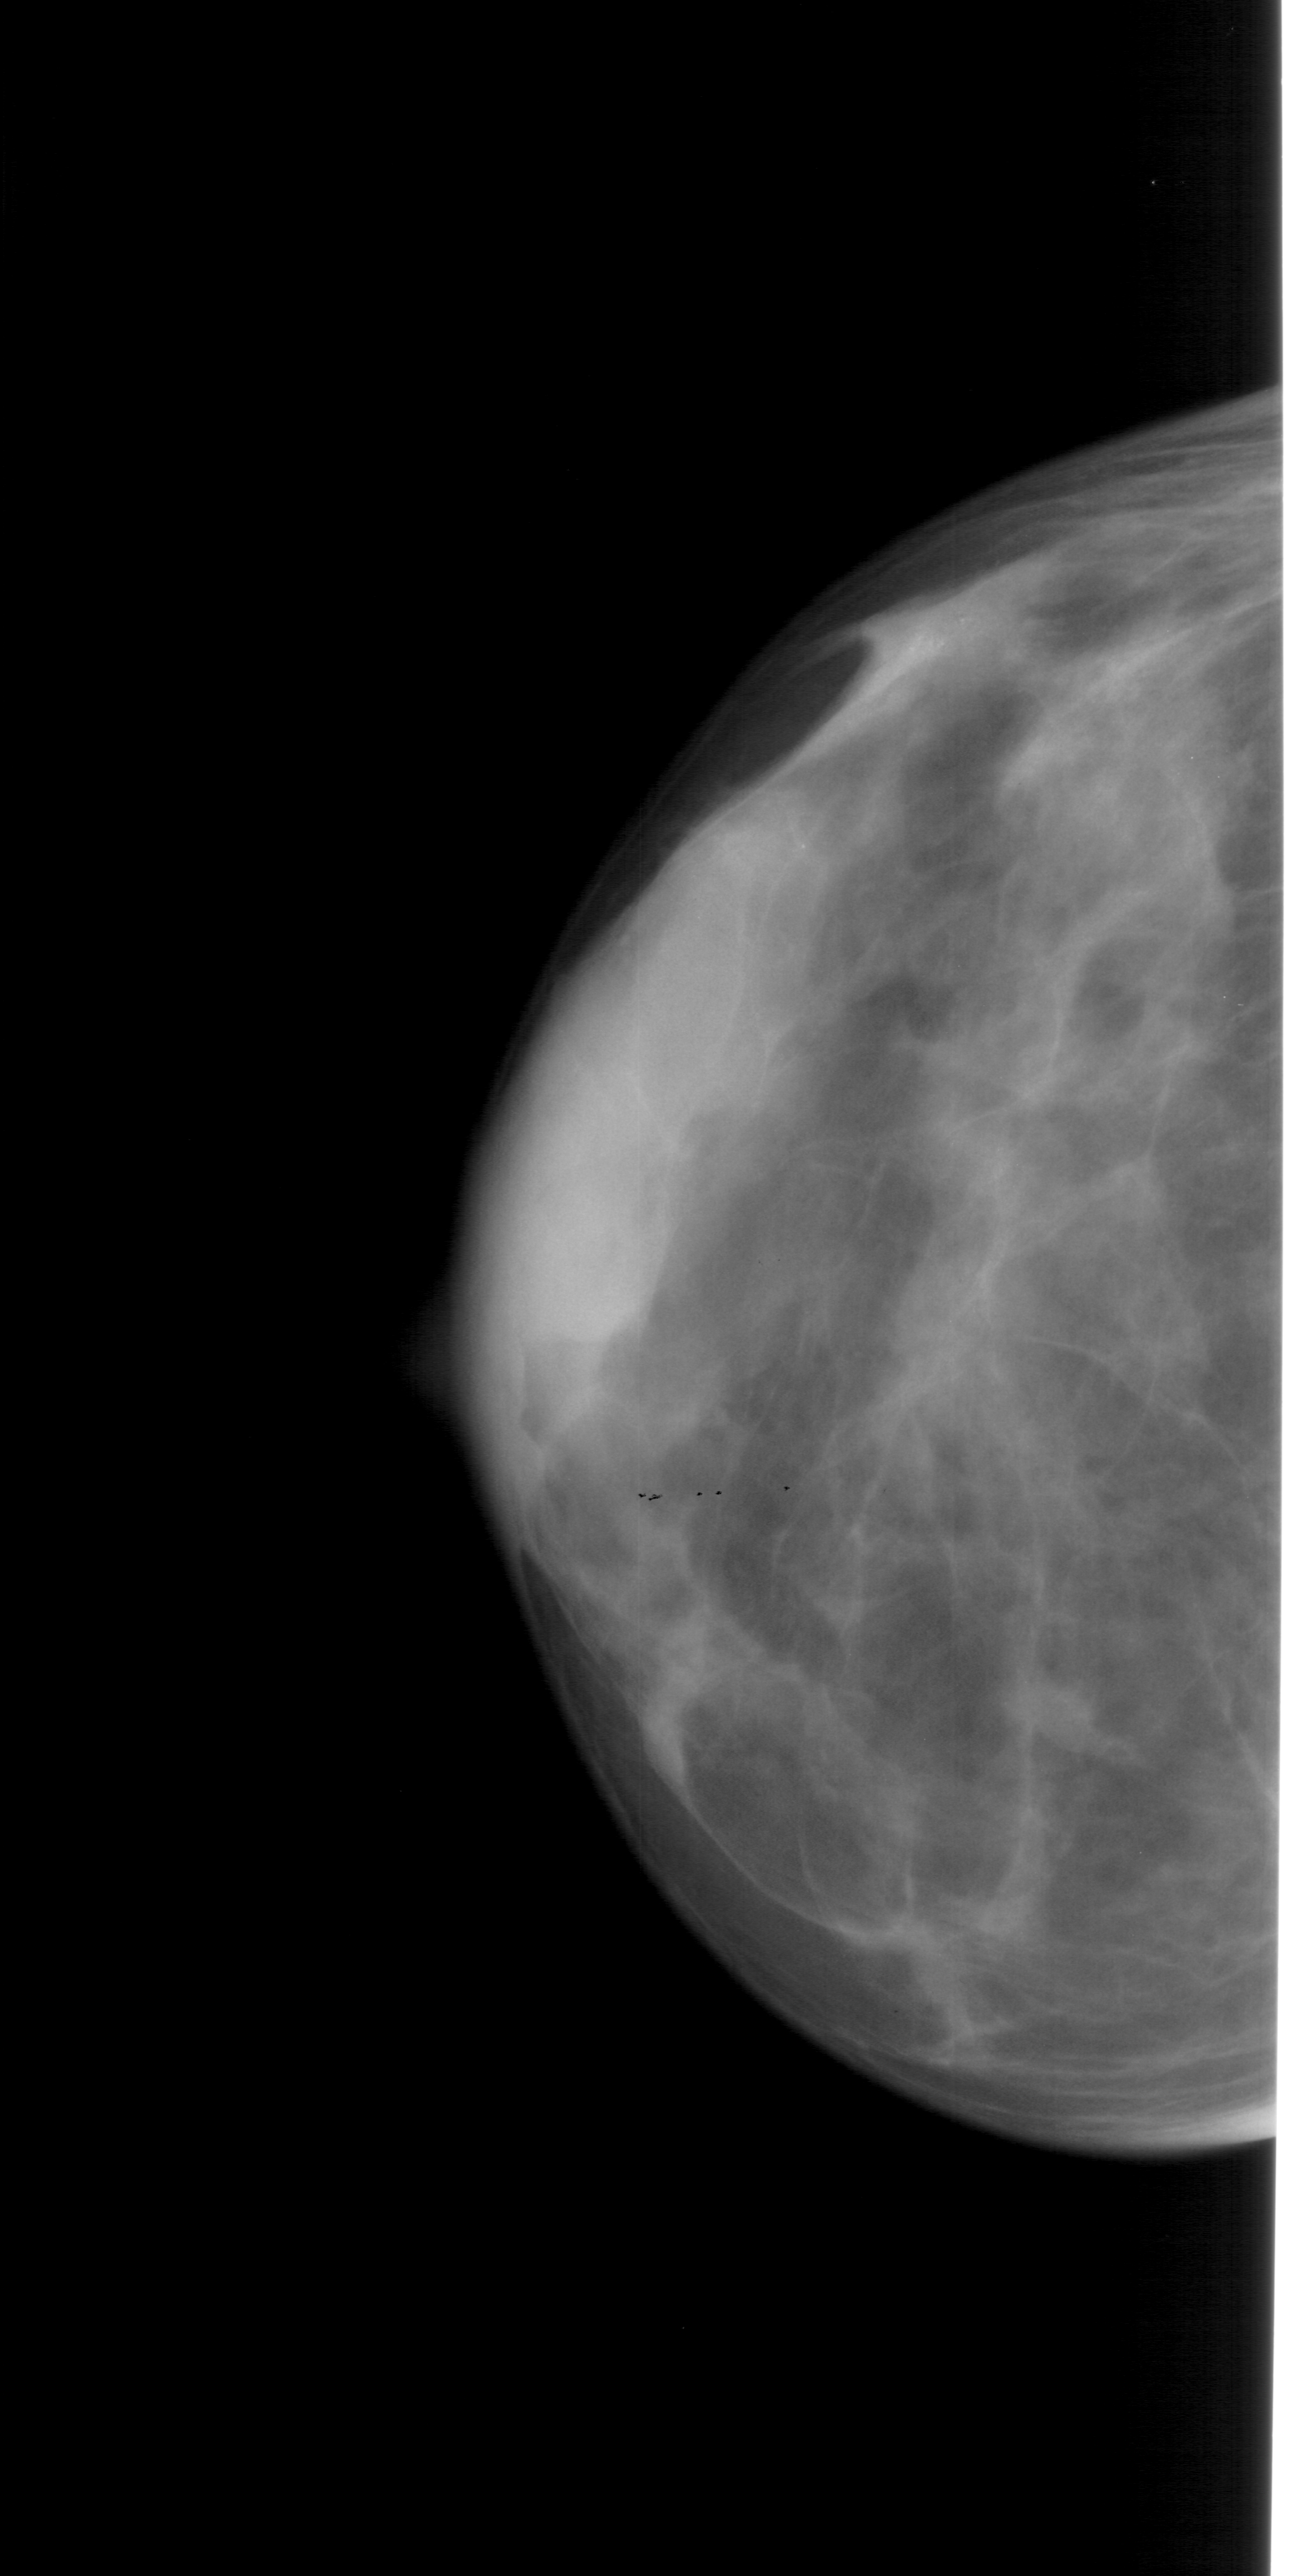
Scanned film-screen mammogram; left breast; craniocaudal (CC) view; BI-RADS breast density category 4 (scale 1–4); 1292 × 2576 image matrix.
Marked abnormalities (boxes around the expert regions of interest):
- calcifications, morphology pleomorphic, distribution clustered; BI-RADS assessment category 4; subtlety rating 1 on a 1 (subtle) to 5 (obvious) scale; pathology result (as recorded, not read from the image): benign: box from (x=886, y=588) to (x=1012, y=683) px